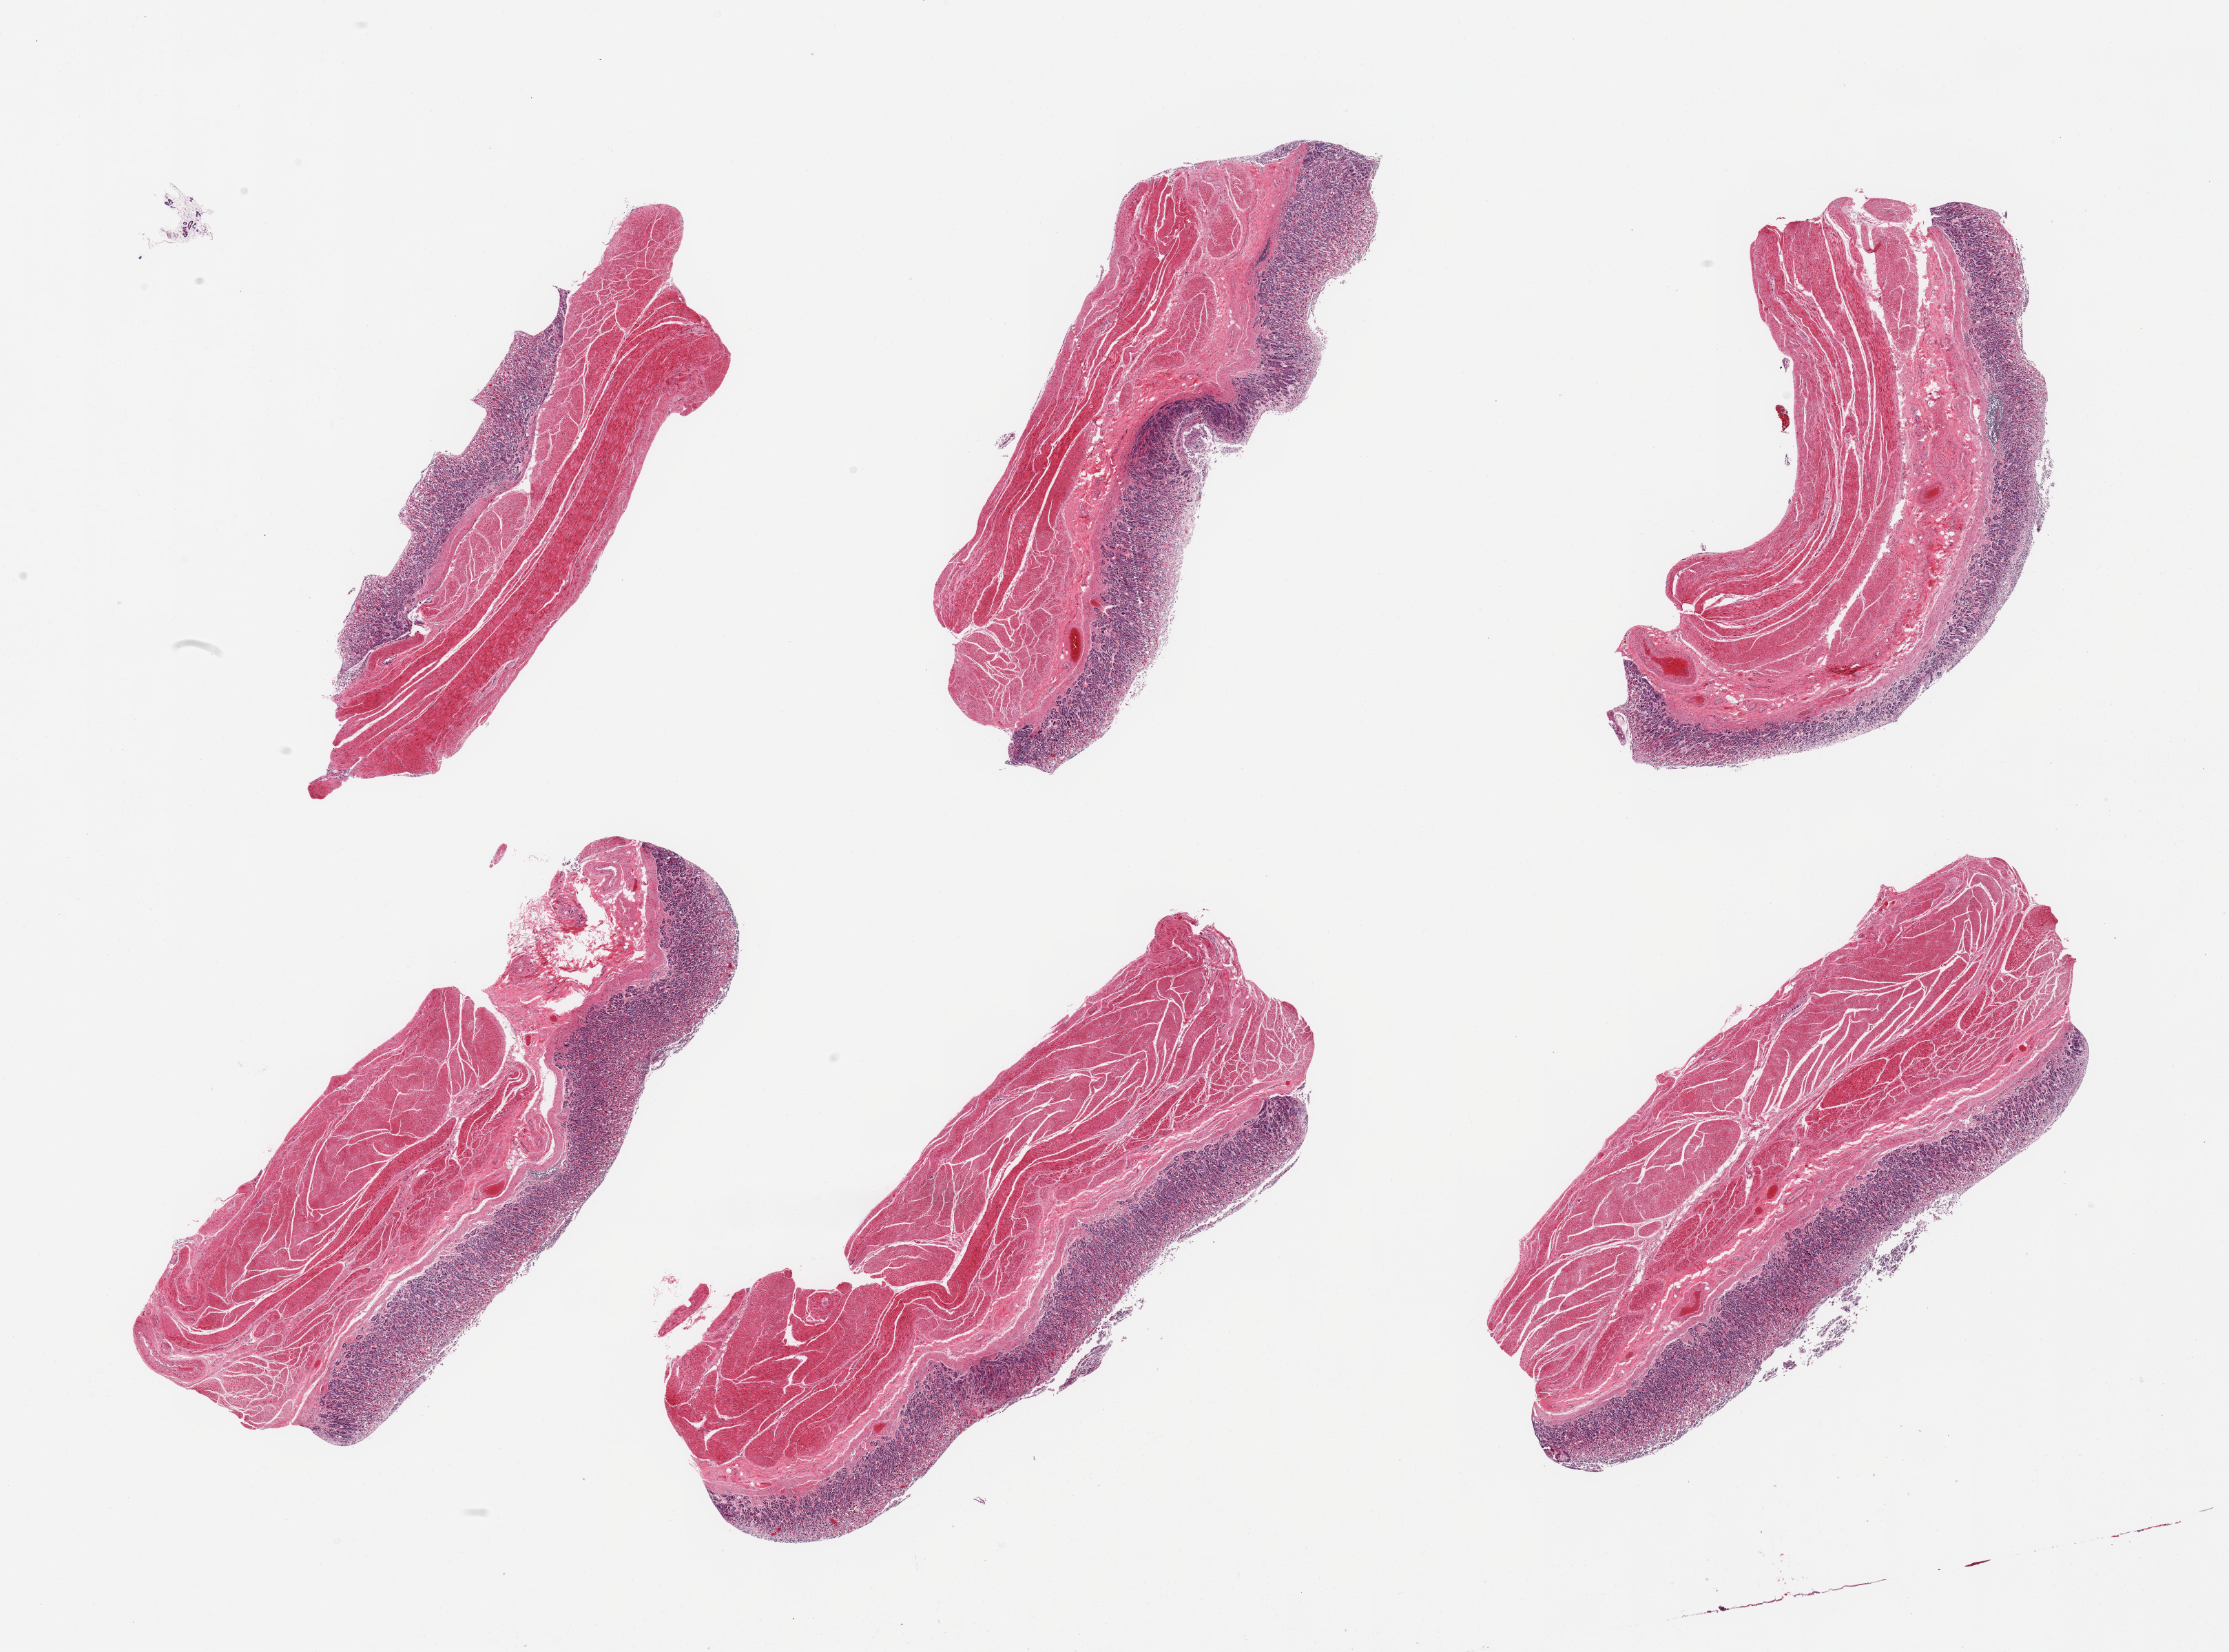
Digitized haematoxylin and eosin-stained section, brightfield — shown as a low-resolution overview of the whole scanned area (about 25.6 x 19.0 mm). PAXgene-fixed, paraffin-embedded tissue. Target tissue: stomach. Tissue donor sample. Female donor.
Pathologist's review note for this sample: 6 pieces; moderate mucosal autolysis, muscularis present.